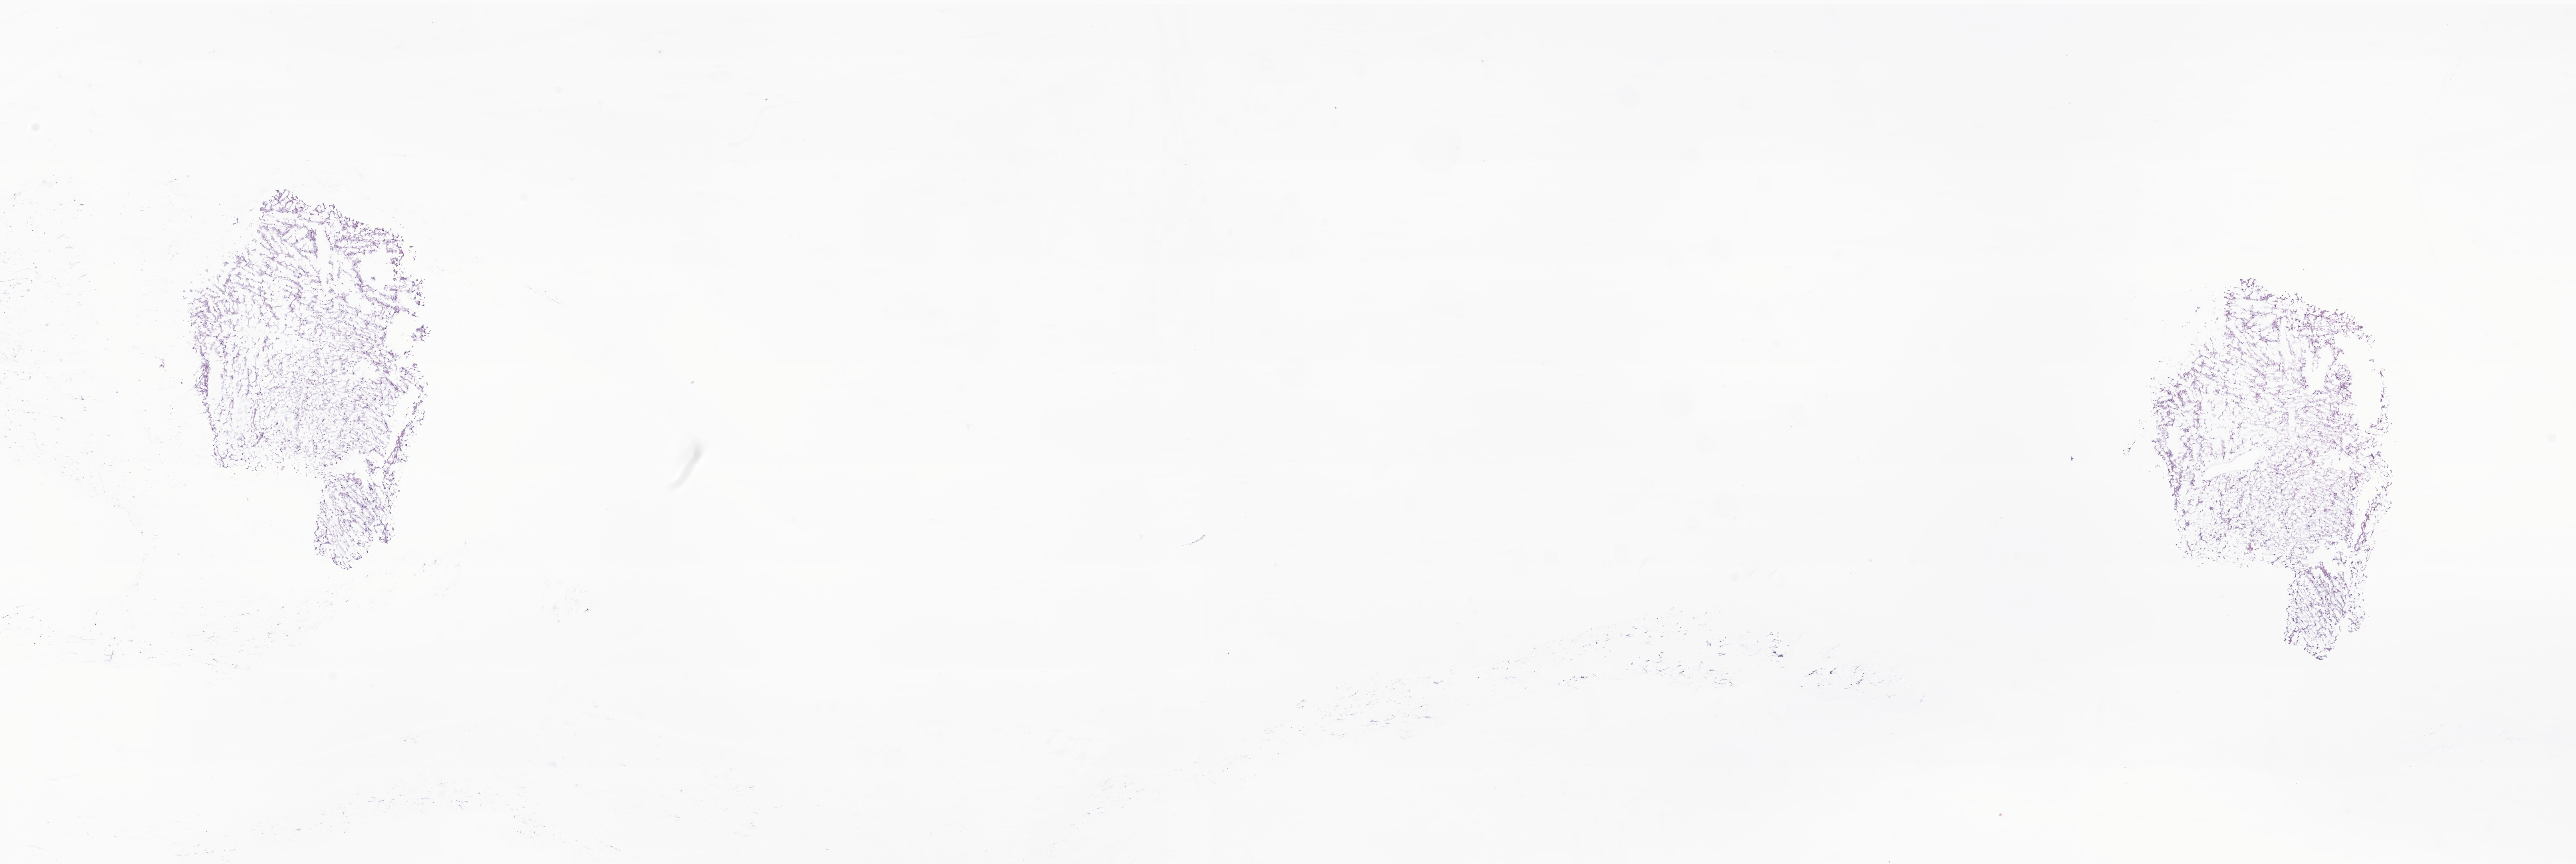
Haematoxylin and eosin whole-slide image of tumor tissue from the brain, a low-resolution overview of the entire scanned area, about 27.2 x 9.1 mm, cryosection (OCT / tissue freezing medium). Patient: female, age 166 months (13 years 10 months).
- diagnosis: Glioma, malignant